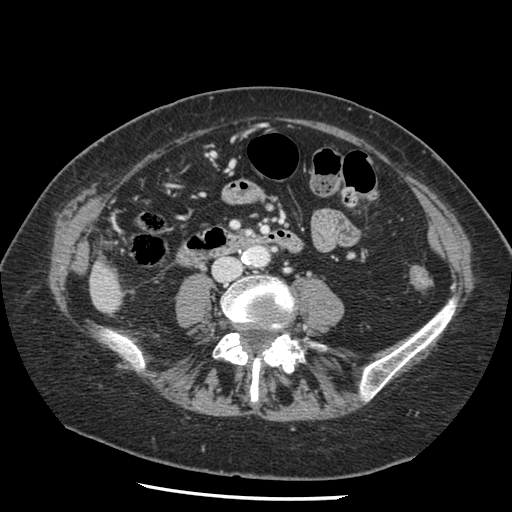
Contrast-enhanced abdominal CT, one axial slice. Position 16 of 148 along the scan axis. Intravenous contrast given. Soft-tissue window (W 400 / L 40 HU). 2.5 mm slice thickness. 512 × 512 image matrix, field of view 330 × 330 mm. Female patient, age 85 years. From the clinical record (not read from this slice): diagnosis: colorectal cancer liver metastases, imaged before liver resection; multiple liver metastases: no; largest metastasis: 0.9 cm; disease in both lobes: no.
Outlined on this slice (outlined manually by an expert reader):
- liver: box from (x=91, y=265) to (x=122, y=313) px
- planned liver remnant (the part of the liver to remain after resection): (x=91, y=265)–(x=122, y=313)